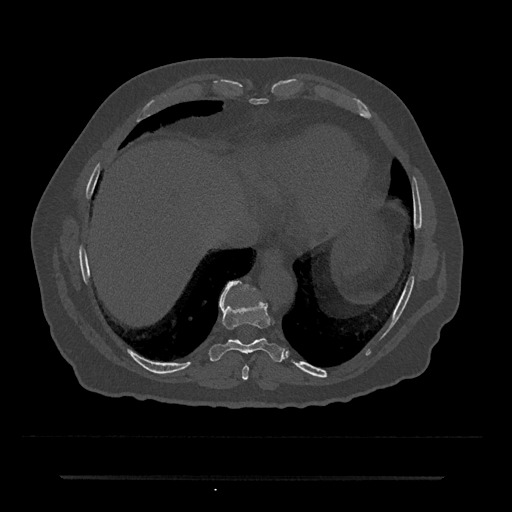
CT including the spine, one axial slice; slice 276 of 797 in the series (ordered by position); bone window (W 1800 / L 400 HU); 0.5 mm slice thickness; 512 × 512 image matrix. Male patient, age 69 years. From the clinical record (not read from this slice): primary cancer: prostate.
Structures marked on this image (semi-automatically segmented with operator editing):
- T10 vertebra: bounding box <244,284,249,290> (left, top, right, bottom; pixels)
- T8 vertebra: <242,365,249,380>
- T9 vertebra: <208,281,285,362>